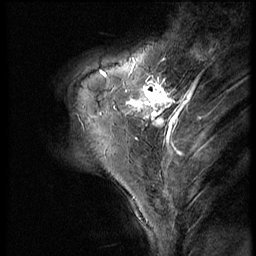
Breast MRI (dynamic contrast-enhanced), one sagittal slice; slice 15 of 56 in the series (ordered by position); 3 images stored at this slice position (order not interpretable as contrast timing); 1.5 T; TE 4.2 ms, TR 9 ms; 2.5 mm slice thickness; 256 × 256 image matrix, field of view 180 × 180 mm. Female patient, age 46 years. Case-level facts recorded for this patient, not image findings: setting: breast cancer imaged before/during neoadjuvant chemotherapy; receptor status: HER2-positive.
Structures marked on this image (semi-automatically segmented with operator editing):
- analysis volume of interest (the breast-tissue region the enhancement analysis was run in; not a lesion): box from (x=79, y=68) to (x=190, y=143) px
- tumour enhancement mask (voxels above the 140 % enhancement threshold inside the analysis volume of interest): (x=100, y=71)–(x=187, y=130)